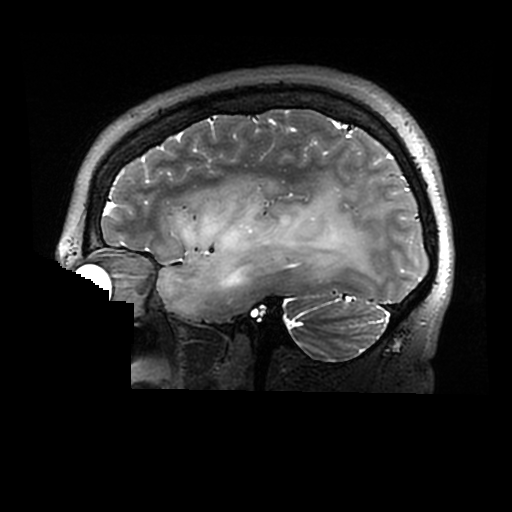
Brain MRI from a brain-tumour surgery series, one sagittal slice. Slice 213 of 320 in the series (ordered by position). 0.6 mm slice thickness. 512 × 512 image matrix, field of view 240 × 240 mm. Case-level facts recorded for this patient, not image findings: histopathology: Astrocytoma; WHO grade: 2; IDH mutation: yes.
Structures marked on this image (expert manual segmentation):
- tumour: box from (x=157, y=182) to (x=379, y=314) px